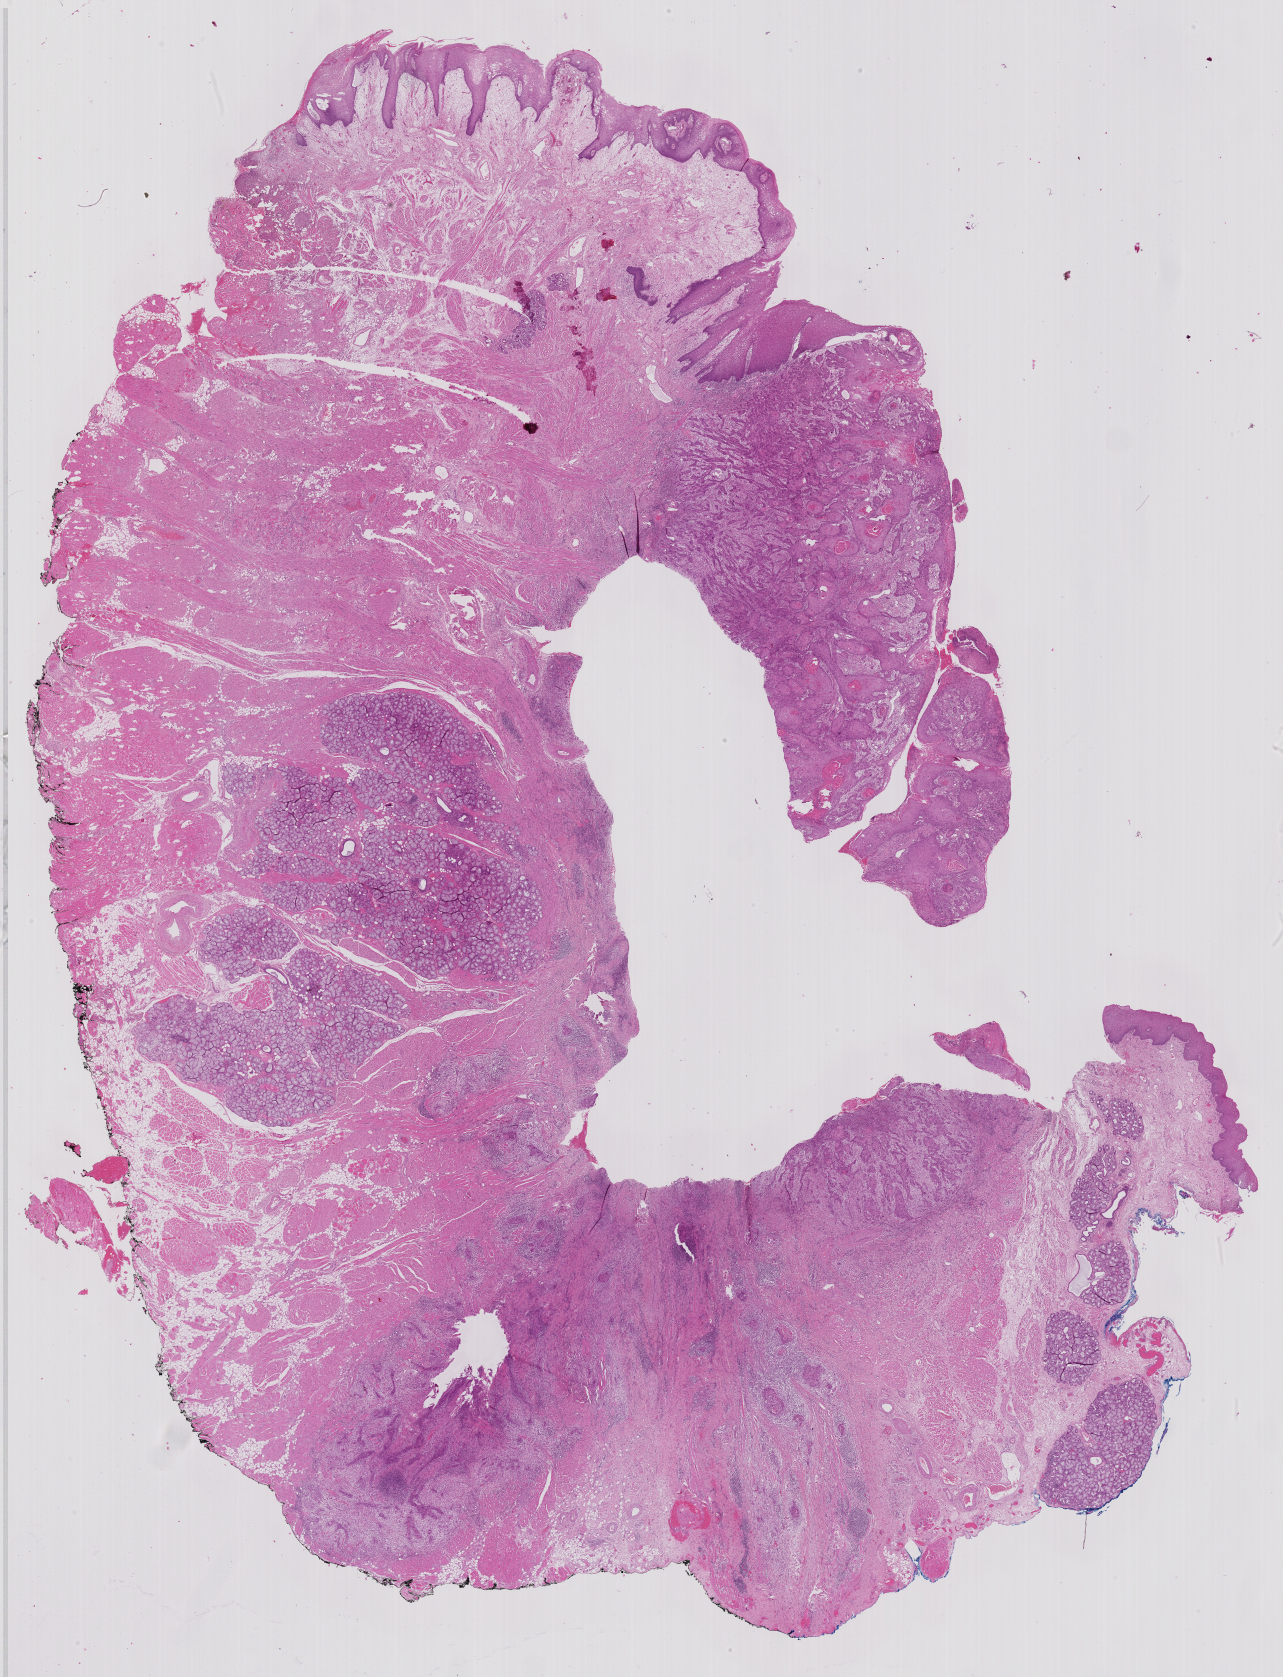
H&E-stained whole-slide image, a low-resolution overview of the entire scanned area, about 20.5 x 26.8 mm; formalin-fixed paraffin-embedded (FFPE) diagnostic section; primary tumour sample from the head and neck. Patient: male, age at initial diagnosis 69 years.
Histologic diagnosis: Squamous cell carcinoma, keratinizing, NOS (tongue, NOS).